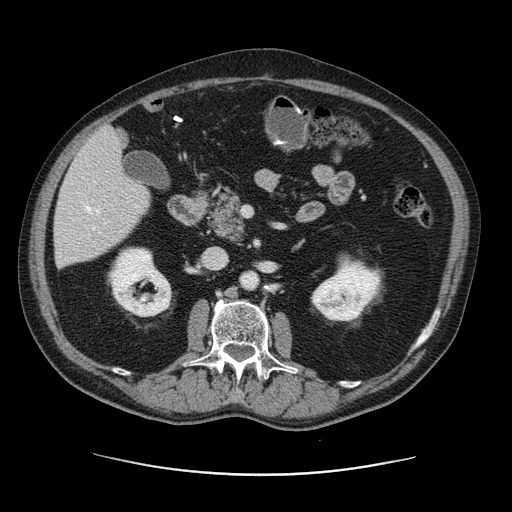
Contrast-enhanced abdominal CT, one axial slice; slice 53 of 141 in the series (ordered by position); 120 kVp; intravenous contrast given; soft-tissue window (W 400 / L 40 HU); 512 × 512 image matrix, field of view 395 × 395 mm. Male patient, age 72 years. Case-level facts recorded for this patient, not image findings: diagnosis: colorectal cancer liver metastases, imaged before liver resection.
Annotated regions visible in this slice (outlined manually by an expert reader):
- hepatic veins: bounding box (x1, y1, x2, y2) in pixels: (85, 206, 100, 230)
- liver: (54, 128, 149, 266)
- planned liver remnant (the part of the liver to remain after resection): (54, 175, 150, 266)